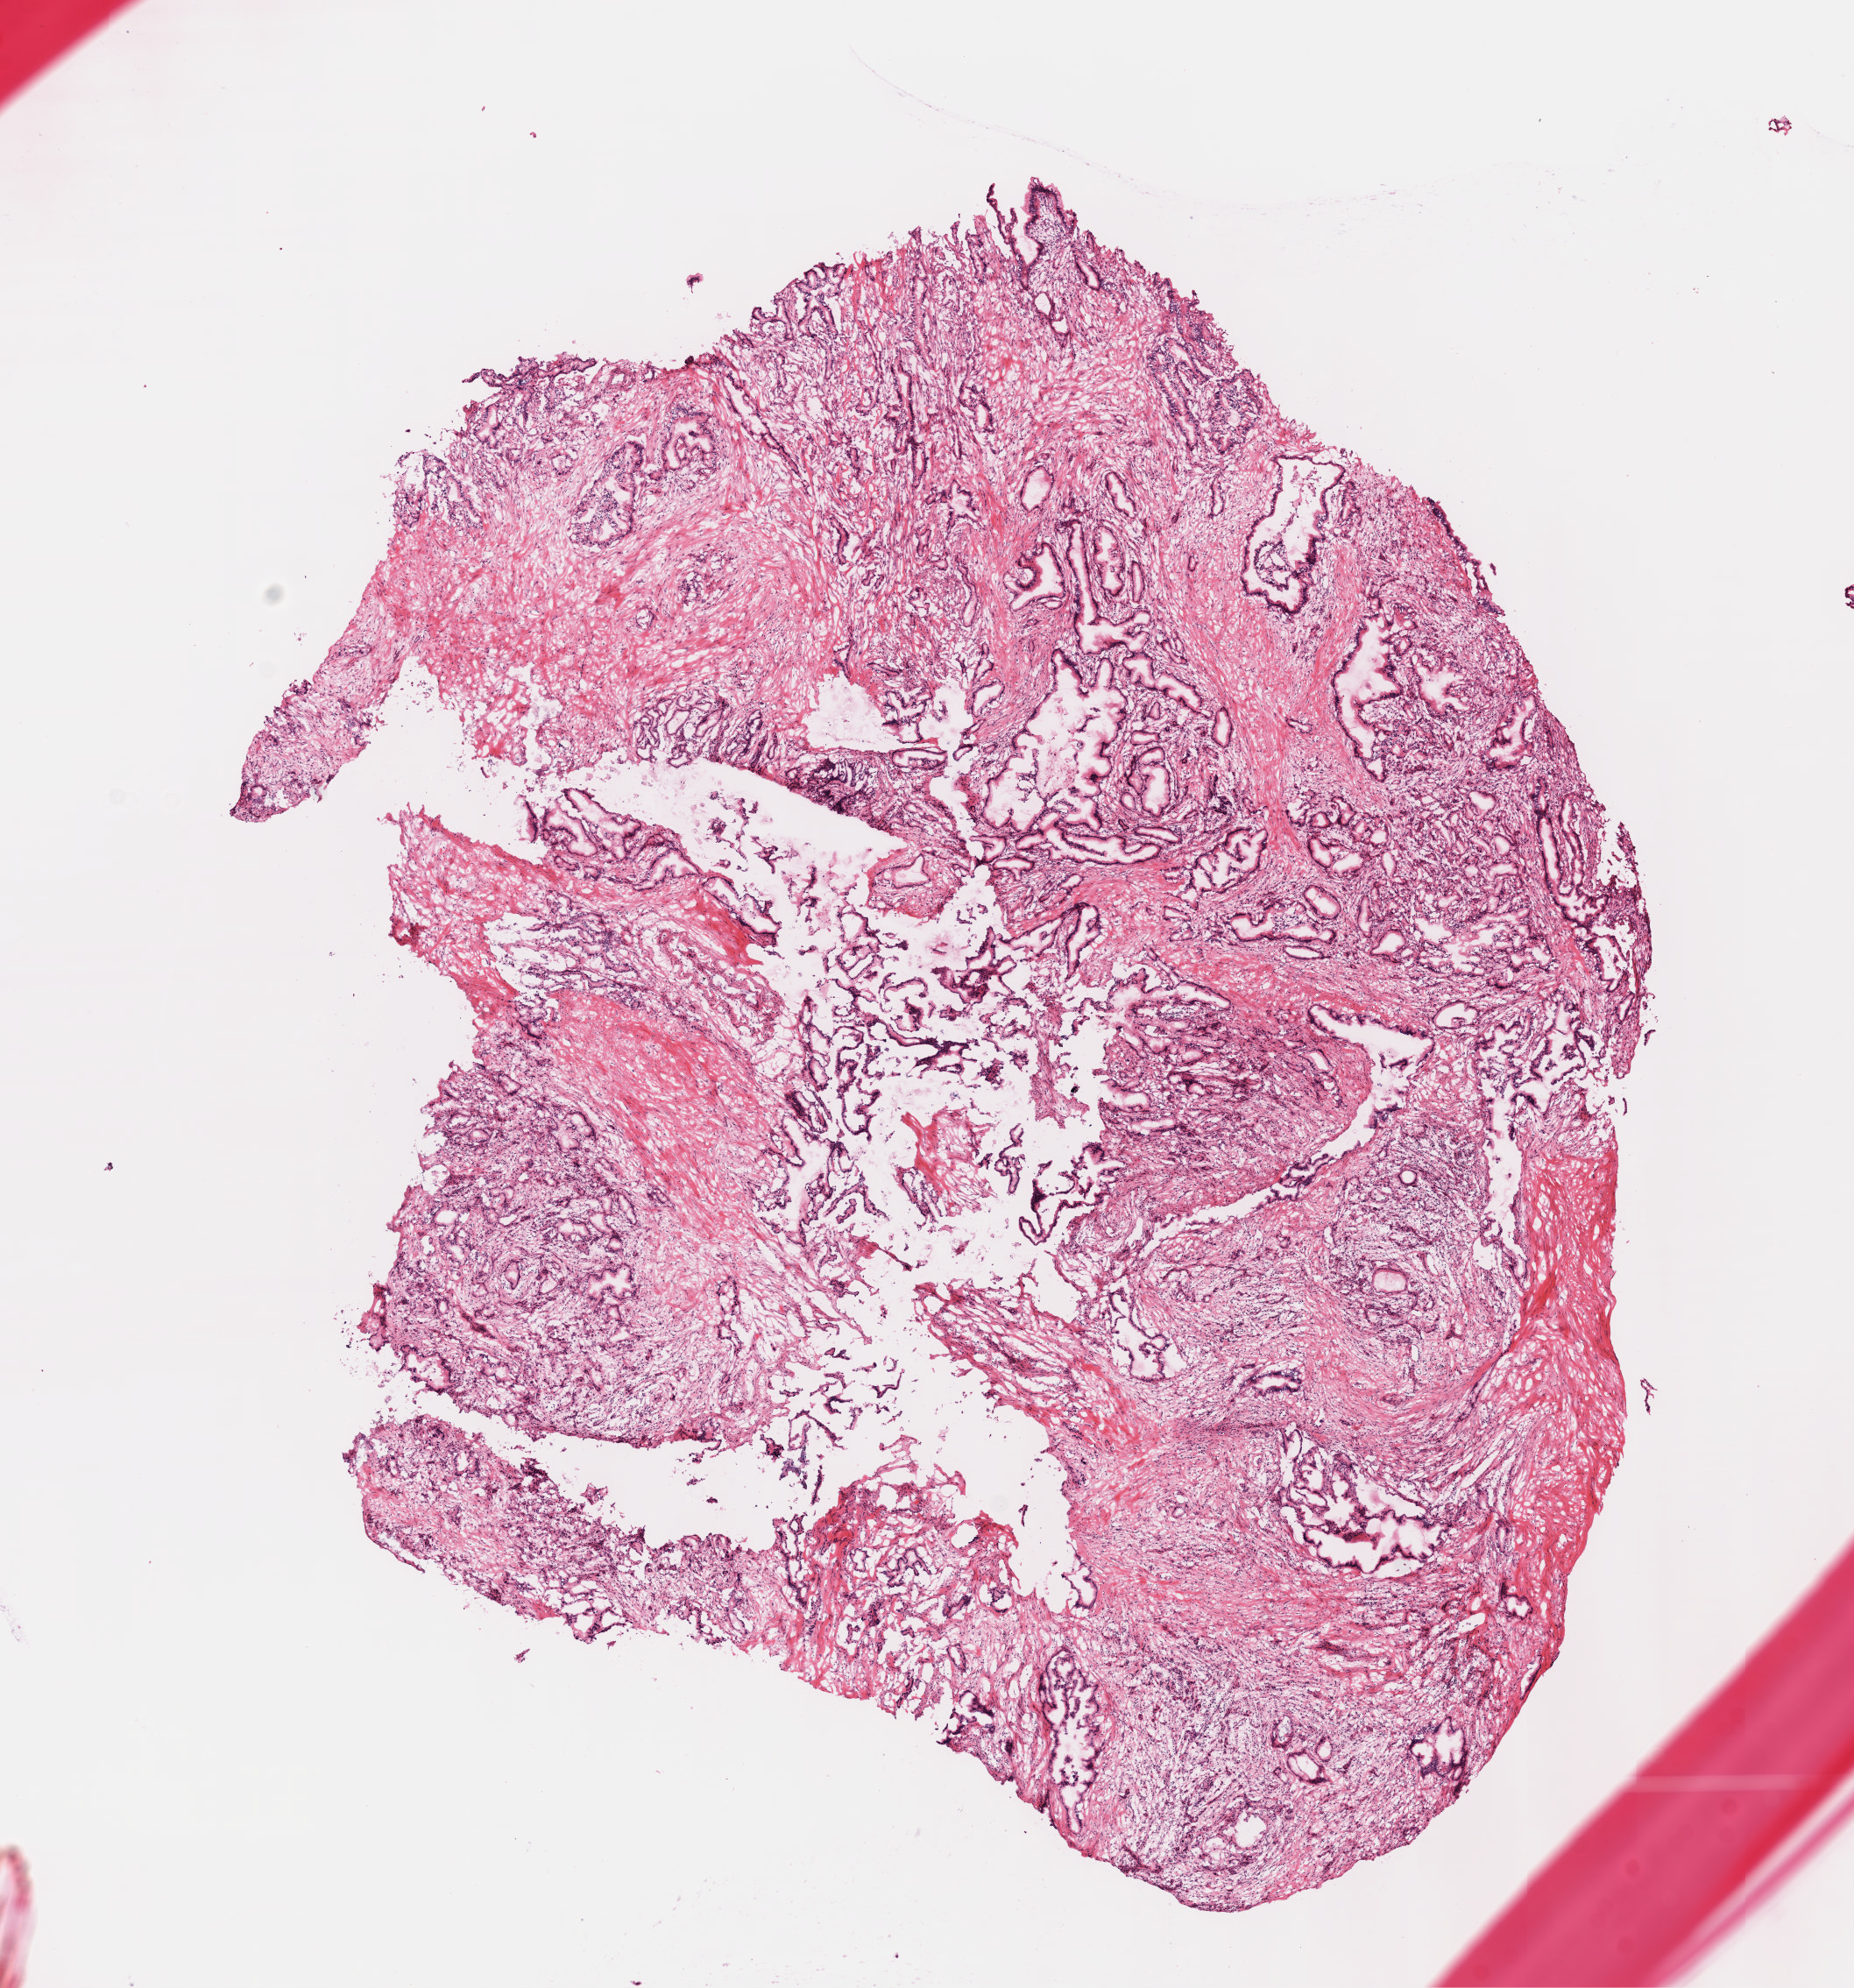
H&E whole-slide image, shown as a low-resolution overview of the whole scanned area (about 8.6 x 9.2 mm, slide scanned at 40x), formalin-fixed paraffin-embedded (FFPE) diagnostic section, primary tumour sample from the pancreas. Female, age 65 years at initial diagnosis. Histologic grade: G2 (moderately differentiated).
AJCC pathologic stage: IIB (7th edition). Lymph nodes positive (case pathology): 1 of 23 examined. Pathologic diagnosis: Infiltrating duct carcinoma, NOS (head of pancreas).